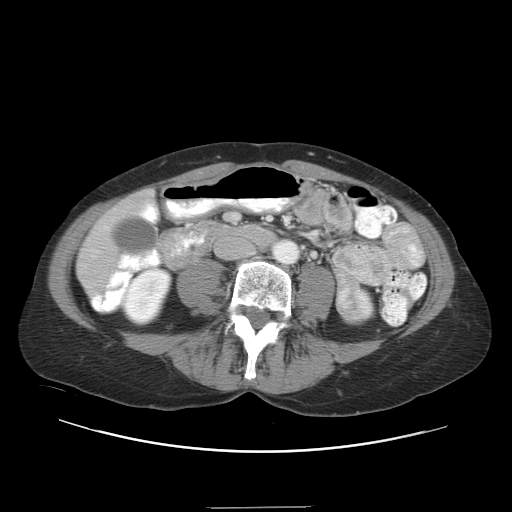
Contrast-enhanced abdominal CT, one axial slice. Position 5 of 38 along the scan axis. Reconstruction kernel STANDARD. 120 kVp. Intravenous contrast given. Soft-tissue window (W 400 / L 40 HU). 5 mm slice thickness. 512 × 512 image matrix. Female patient, age 64 years. From the clinical record (not read from this slice): diagnosis: colorectal cancer liver metastases, imaged before liver resection; multiple liver metastases: no; largest metastasis: 3.8 cm; disease in both lobes: yes.
Outlined on this slice (outlined manually by an expert reader):
- hepatic veins: box from (x=105, y=227) to (x=107, y=229) px
- liver: (x=79, y=197)–(x=148, y=291)